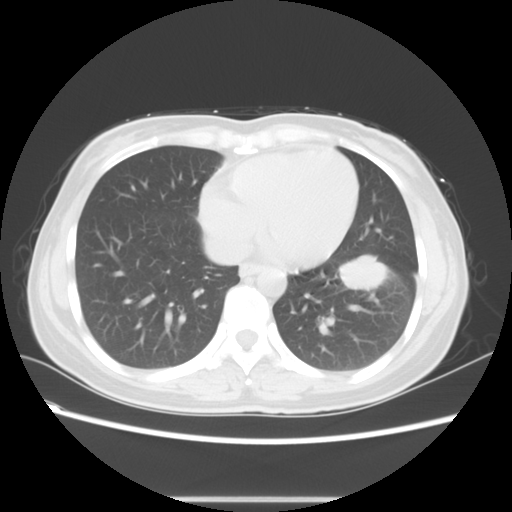
Chest CT, one axial slice. Slice 22 of 56 in the series (ordered by position). Reconstruction kernel STANDARD. Lung window (W 1500 / L -600 HU). 5 mm slice thickness. 512 × 512 image matrix, field of view 350 × 350 mm. Patient: female, 41 years. Case-level facts recorded for this patient, not image findings: clinical TNM (as recorded): T1c N3 M1b.
Outlined on this slice (bounding box drawn by a radiologist):
- lung tumour (recorded histology: adenocarcinoma): bounding box <332,248,400,307> (left, top, right, bottom; pixels)